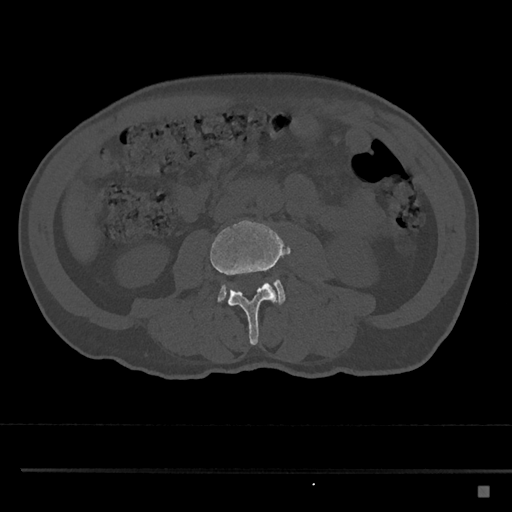
CT including the spine, one axial slice. Position 681 of 797 along the scan axis. Reconstruction kernel Br40s/3. Bone window (W 1800 / L 400 HU). 512 × 512 image matrix, field of view 391 × 391 mm. Patient: male, 59 years. Case-level facts recorded for this patient, not image findings: primary cancer: prostate.
Annotated regions visible in this slice (semi-automatically segmented with operator editing):
- L3 vertebra: bounding box [x1, y1, x2, y2] px = [210, 220, 286, 345]
- L4 vertebra: [217, 279, 286, 305]